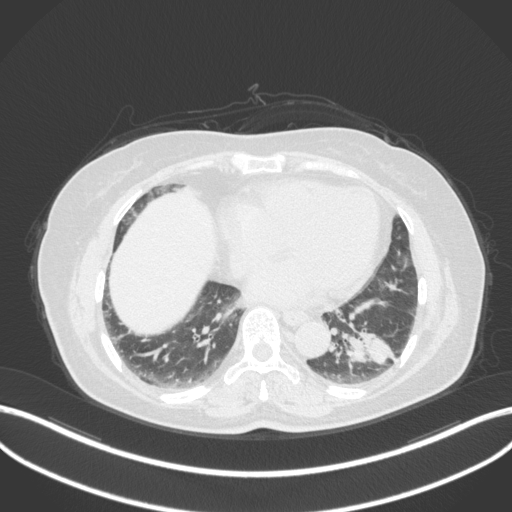
Chest CT, one axial slice; position 136 of 307 along the scan axis; reconstruction kernel B31f; 120 kVp; lung window (W 1500 / L -600 HU); 1 mm slice thickness; 512 × 512 image matrix, field of view 400 × 400 mm. Female patient, age 59 years. Case-level facts recorded for this patient, not image findings: clinical TNM (as recorded): T2a N0 M0; histopathological grade: G2-3.
Annotated regions visible in this slice (rectangle marked by the reading radiologist):
- lung tumour (recorded histology: adenocarcinoma): bounding box [x1, y1, x2, y2] px = [337, 328, 393, 370]